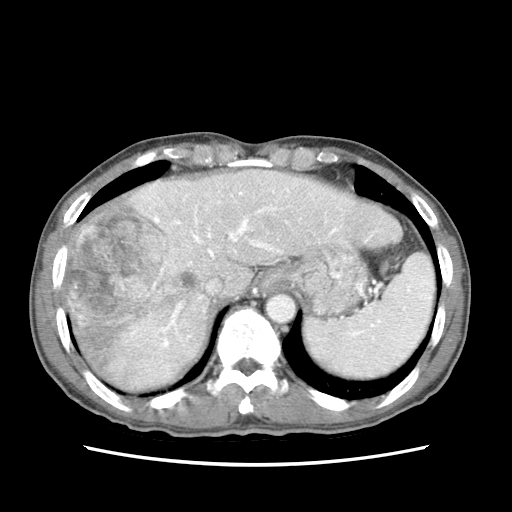
Contrast-enhanced abdominal CT (liver protocol), one axial slice; reconstruction kernel STANDARD; 120 kVp; soft-tissue window (W 400 / L 40 HU); 2.5 mm slice thickness; 512 × 512 image matrix, field of view 320 × 320 mm. From the clinical record (not read from this slice): diagnosis: hepatocellular carcinoma (patient treated with transarterial chemoembolisation; whether this scan precedes or follows treatment is not stated here); TNM stage (as recorded): Stage-IIIB.
Outlined on this slice (semi-automatically segmented with operator editing):
- abdominal aorta: bounding box (x1, y1, x2, y2) in pixels: (266, 293, 294, 322)
- liver parenchyma outside the tumour (the mass and vessels are separate outlines, so this box may not span the whole liver): (60, 170, 400, 390)
- mass: (63, 183, 200, 368)
- liver vessels: (144, 180, 338, 347)